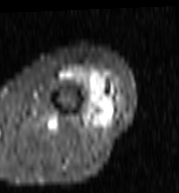
MRI of an extremity soft-tissue mass, one axial slice; position 33 of 103 along the scan axis; STIR; MR volume resampled by the dataset authors to the PET/CT grid (not the native acquisition matrix); 3.27 mm slice thickness; 179 × 193 image matrix, field of view 175 × 188 mm. Female patient. Case-level facts recorded for this patient, not image findings: histological type: undifferentiated – high grade; grade: high; site of the primary tumour: left thigh.
Structures marked on this image (expert contour drawn on MRI and transferred to this co-registered scan by the dataset authors):
- gross tumour volume including surrounding oedema: bounding box [x1, y1, x2, y2] px = [61, 67, 119, 118]